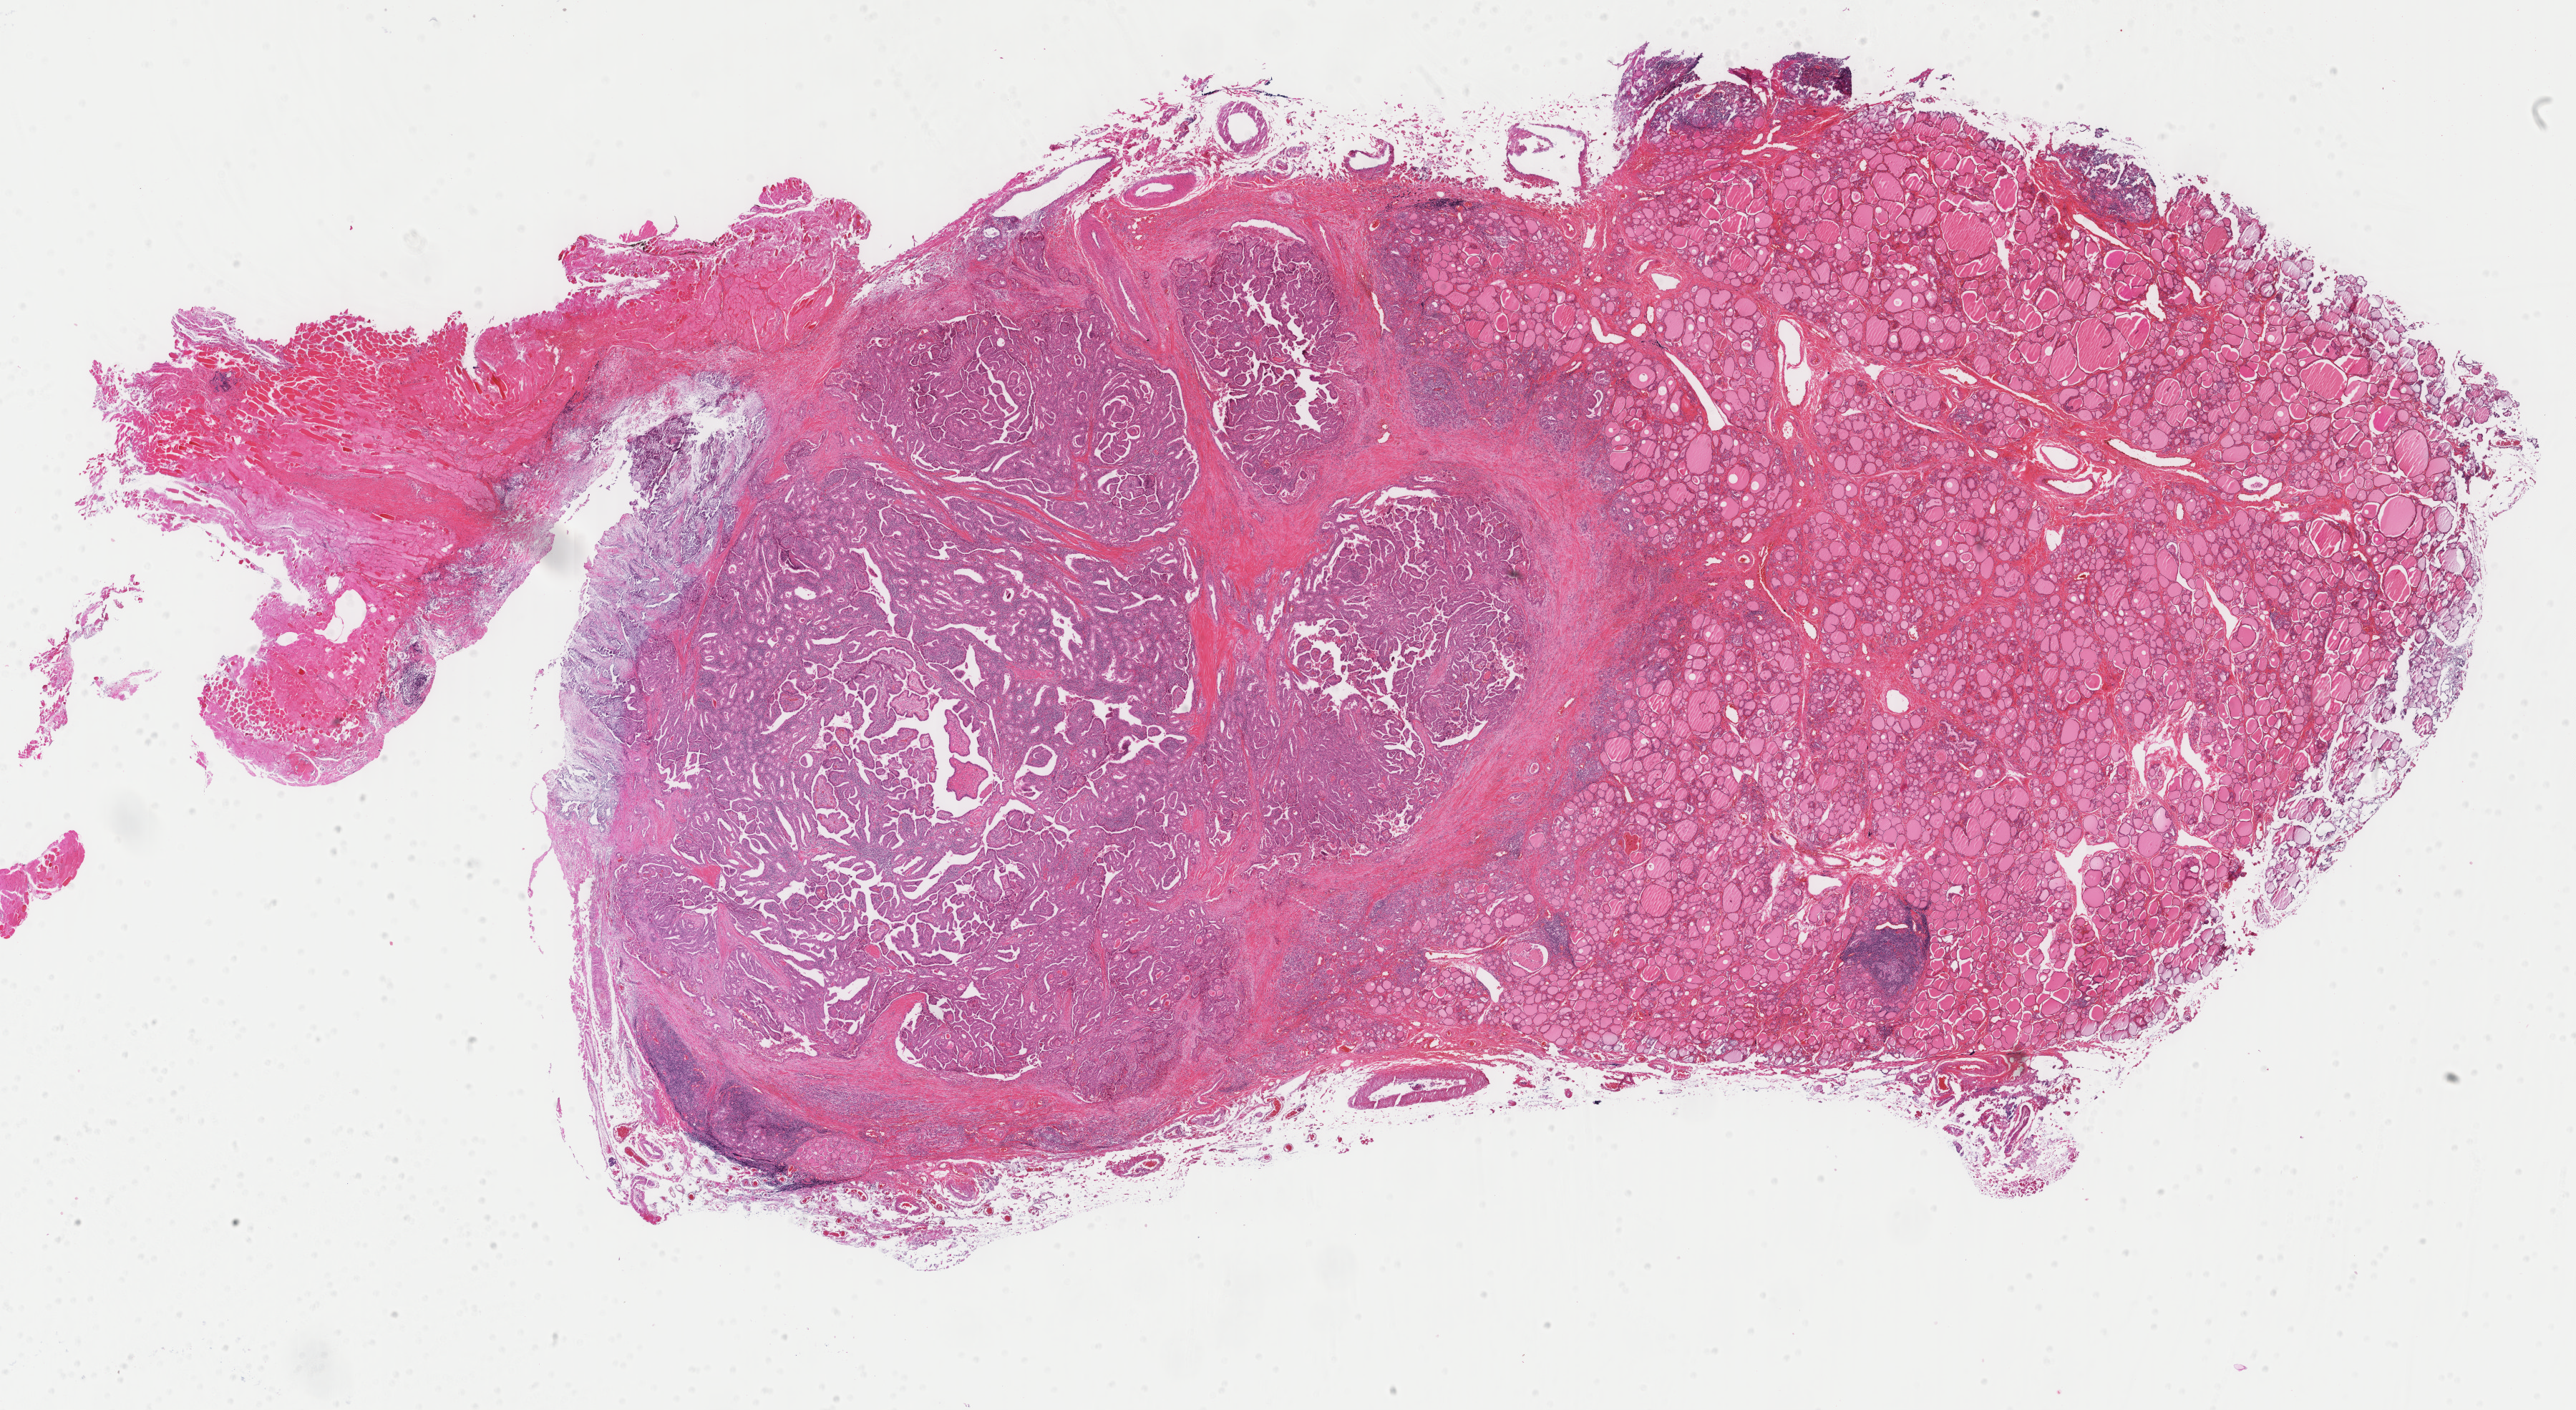
Whole-slide histology image, H&E — low-resolution overview of the scanned area, about 28.6 x 15.6 mm. Formalin-fixed paraffin-embedded (FFPE) diagnostic section. Sample: primary tumour, thyroid. Female patient; age at initial diagnosis 47 years.
Lymph nodes positive (case pathology): 0 of 1 examined. Laterality: left. Diagnosis: Papillary adenocarcinoma, NOS (thyroid gland). TNM: T3 N0 M0. AJCC pathologic stage: II (5th edition).